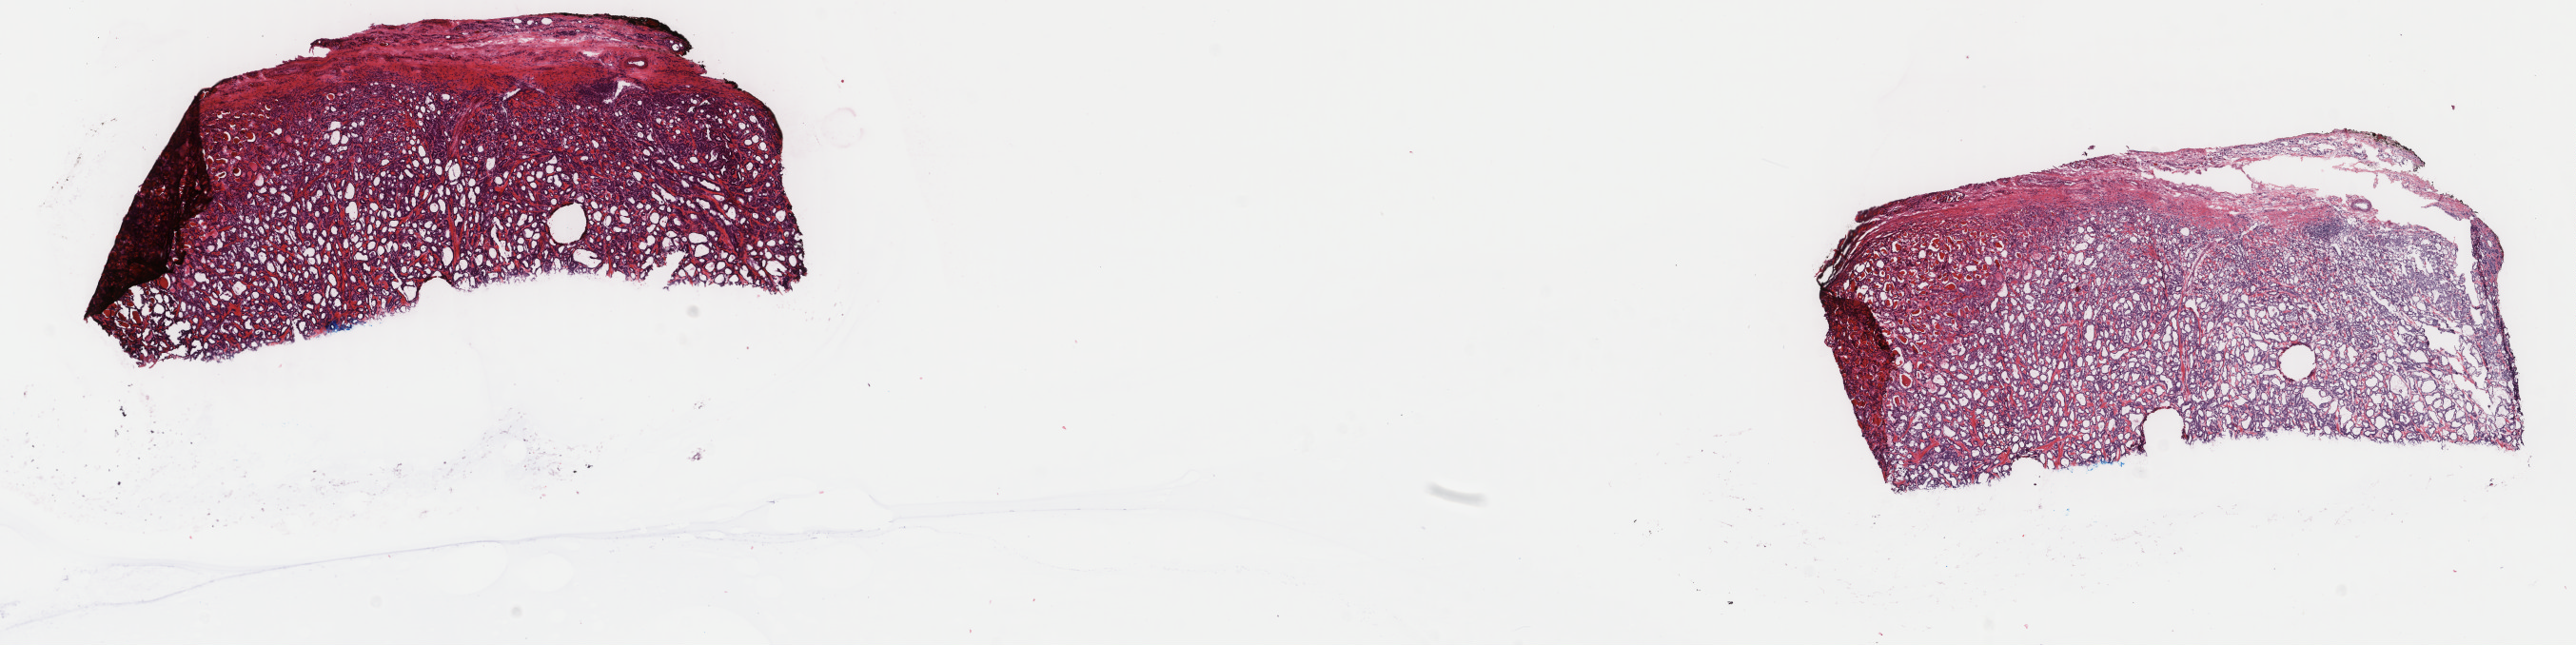
H&E whole-slide image — shown as a low-resolution overview of the whole scanned area (about 21.5 x 5.4 mm). Frozen section from the top of the tissue portion. Thyroid, primary tumour sample. Female patient; age at initial diagnosis 55 years. Slide review estimates, as recorded: tumour cells 80%, tumour nuclei 95%, normal cells 5%, stromal cells 15%, necrosis 0%. Inflammatory infiltration, as recorded: lymphocyte infiltration 1%, monocyte infiltration 1%, neutrophil infiltration 0%.
Diagnosis: Papillary carcinoma, follicular variant. AJCC pathologic stage: I. Lymph nodes positive (case pathology): 0 of 3 examined.